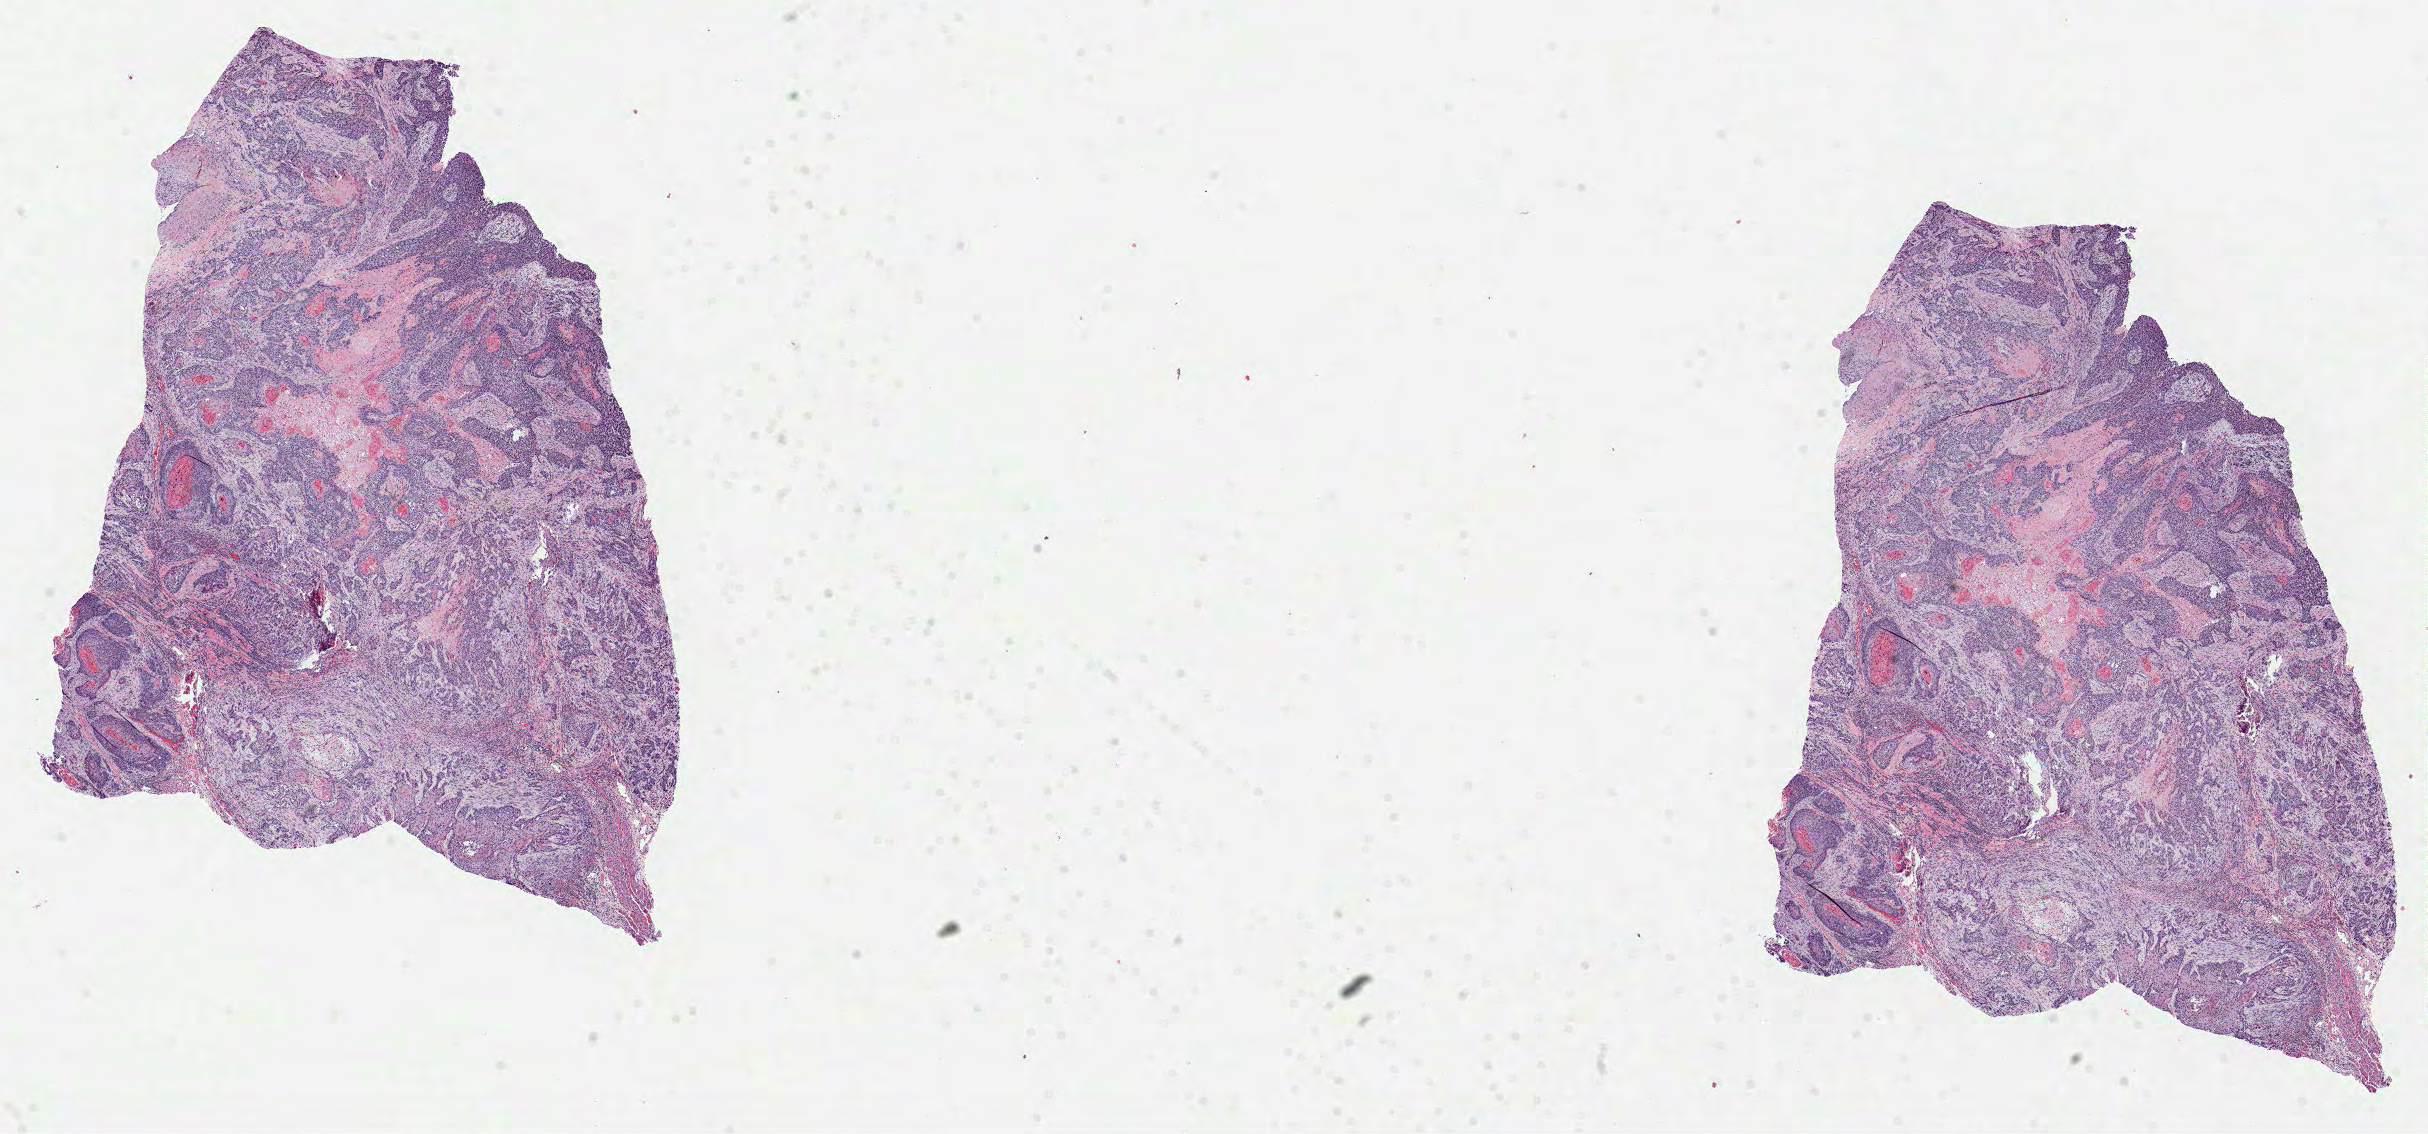
Whole-slide histology image, Hematoxylin and eosin (H&E) stained — shown as a low-resolution overview of the whole scanned area (about 19.6 x 9.1 mm, from a 40x scan), formalin-fixed paraffin-embedded (FFPE) diagnostic section, primary tumour sample from the head and neck. Male patient; age at initial diagnosis 66 years. Histologic grade: G2 (moderately differentiated).
AJCC pathologic stage: IVA (6th edition). Histologic diagnosis: Squamous cell carcinoma, NOS (tongue, NOS).